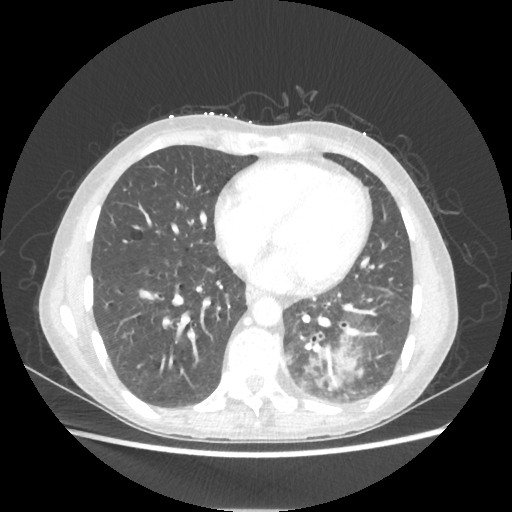
Chest CT, one axial slice. Slice 84 of 221 in the series (ordered by position). Reconstruction kernel STANDARD. 80 kVp. Lung window (W 1500 / L -600 HU). 512 × 512 image matrix, field of view 360 × 360 mm. Female patient, age 53 years. From the clinical record (not read from this slice): clinical TNM (as recorded): T3 N0 M0.
Outlined on this slice (bounding box drawn by a radiologist):
- lung tumour (recorded histology: adenocarcinoma): box from (x=308, y=338) to (x=358, y=373) px